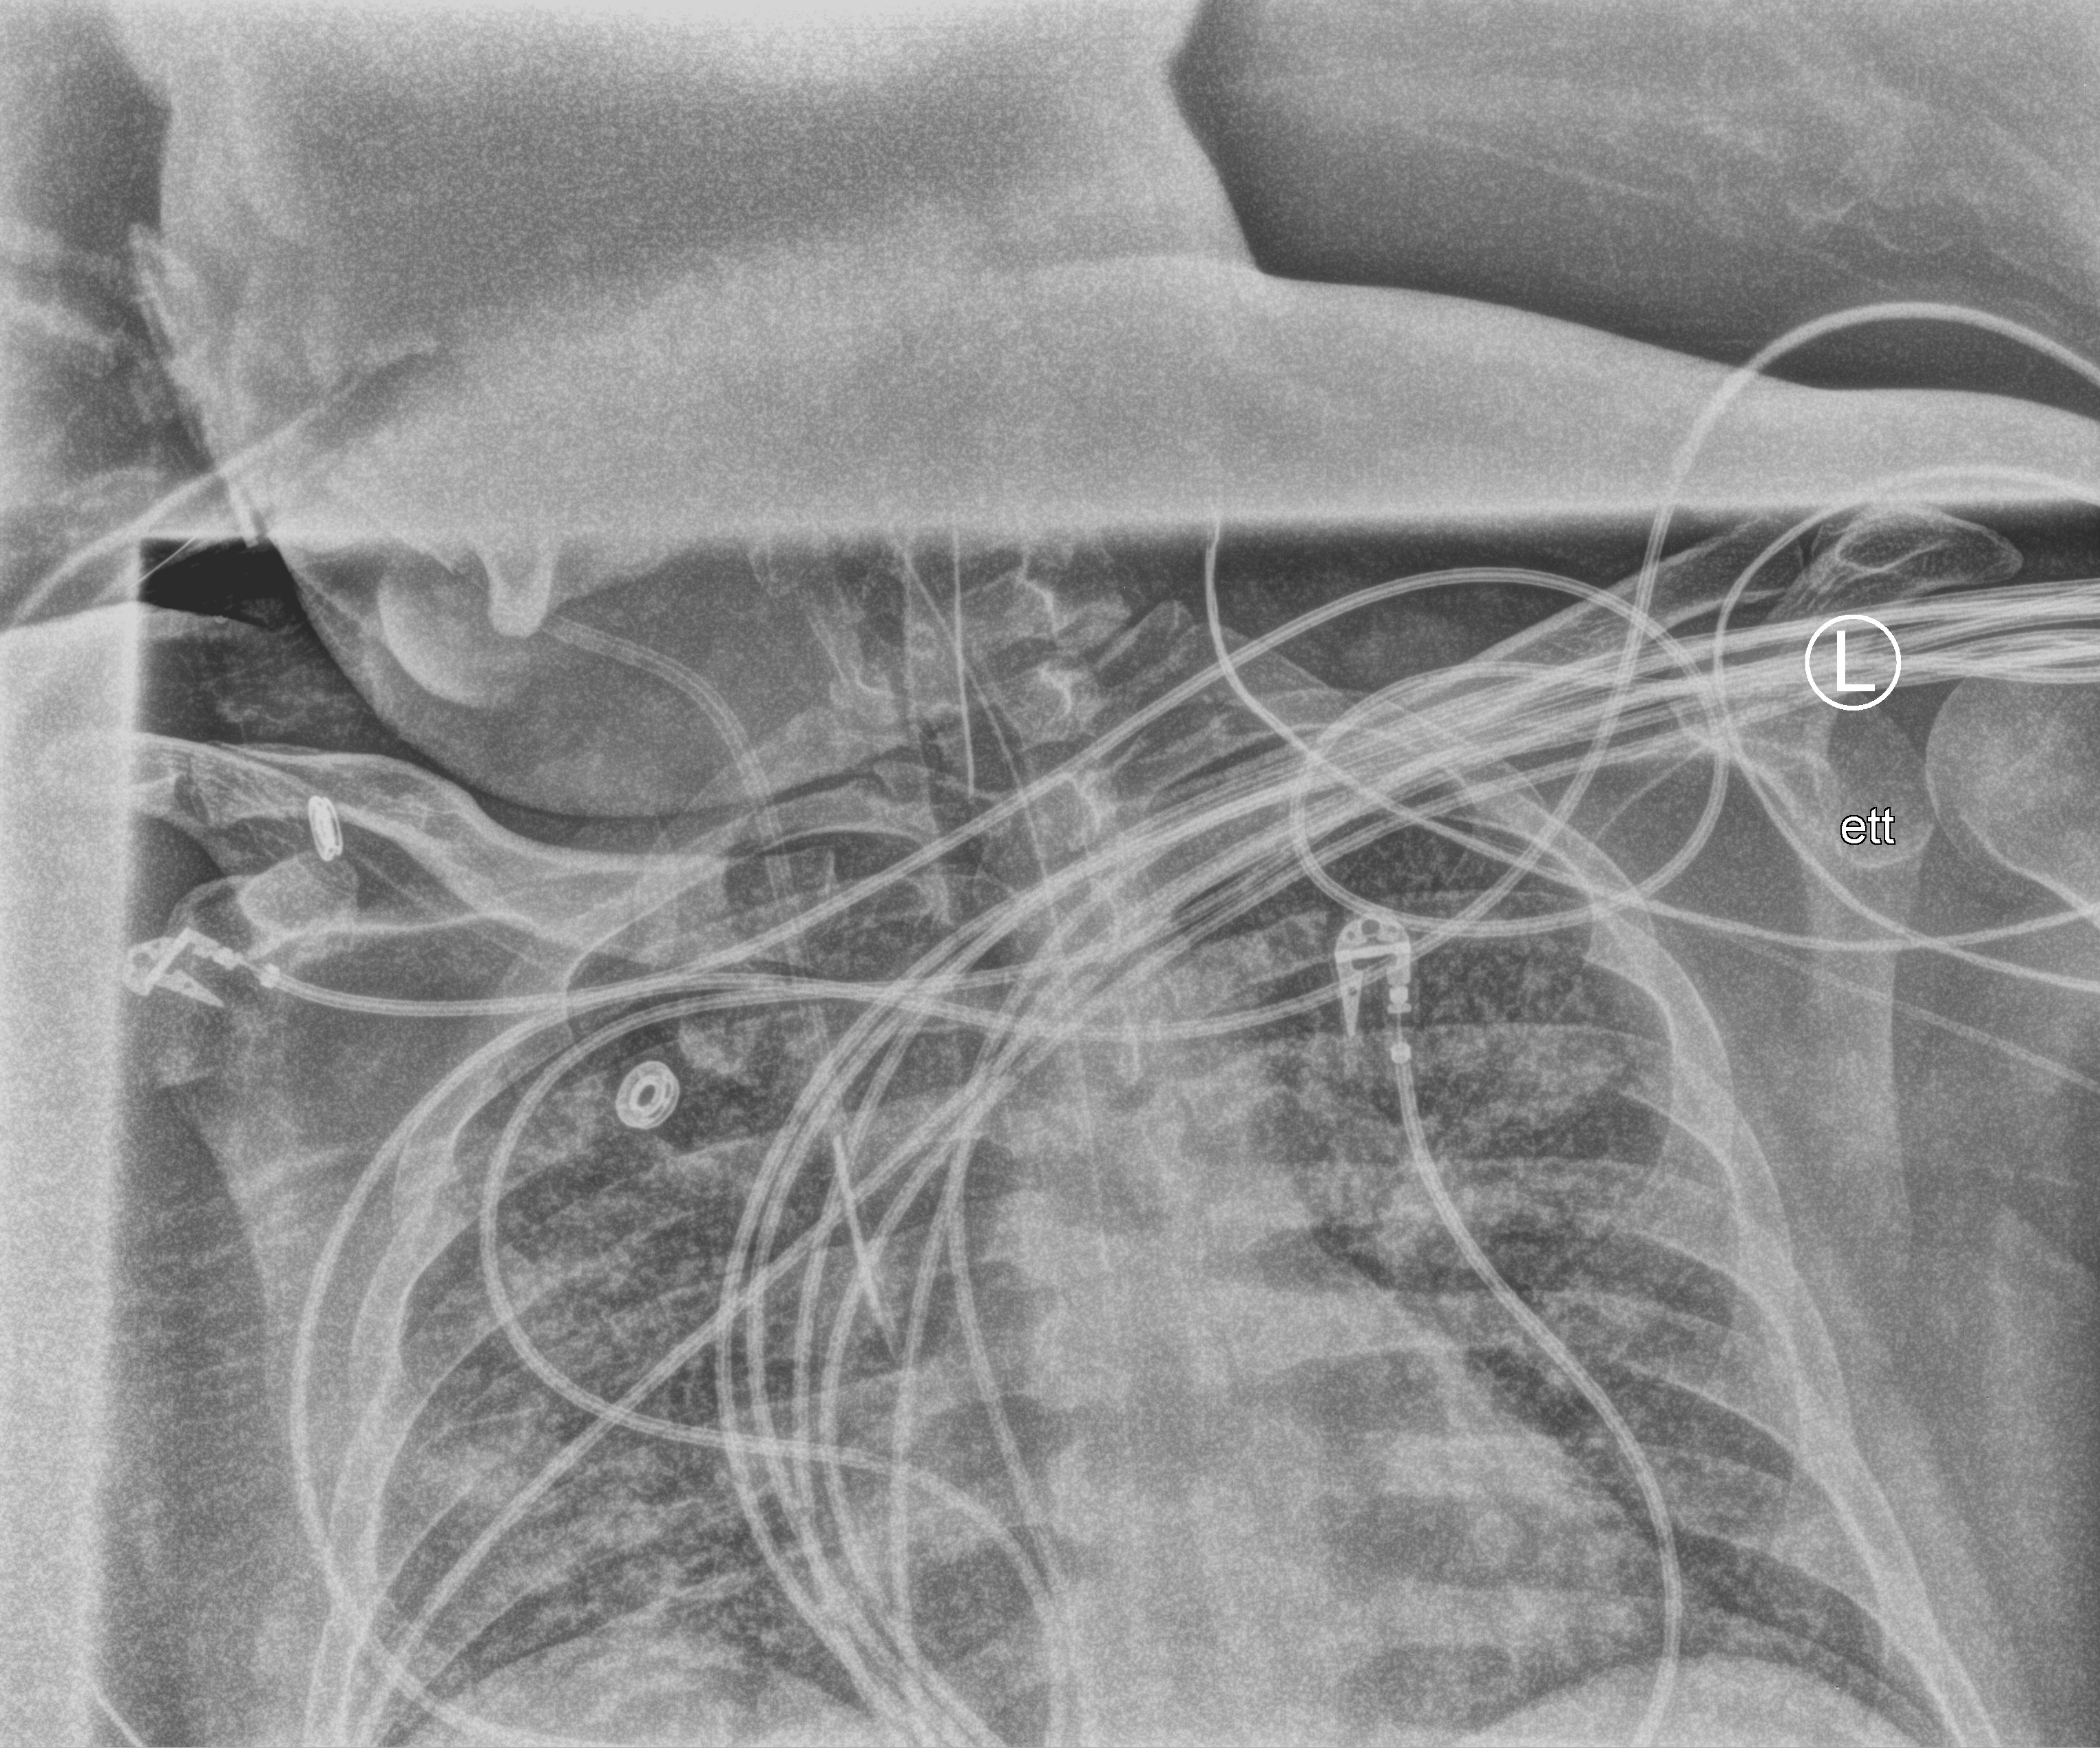
Bedside chest radiograph (computed radiography); anteroposterior (AP) projection. Adult patient hospitalised with COVID-19, age 18–59 years.
From the hospital-stay record, not from the radiograph (when in the stay this image was taken is not recorded):
- admitted to intensive care during this hospital stay: yes